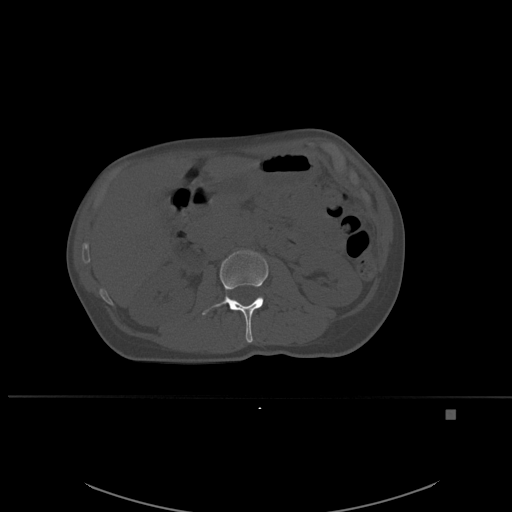
CT including the spine, one axial slice; position 234 of 537 along the scan axis; bone window (W 1800 / L 400 HU); 1.5 mm slice thickness; 512 × 512 image matrix, field of view 440 × 440 mm. Patient: female, 45 years. From the clinical record (not read from this slice): primary cancer: lung.
Structures marked on this image (semi-automatically segmented with operator editing):
- L2 vertebra: bounding box (x1, y1, x2, y2) in pixels: (201, 250, 269, 343)